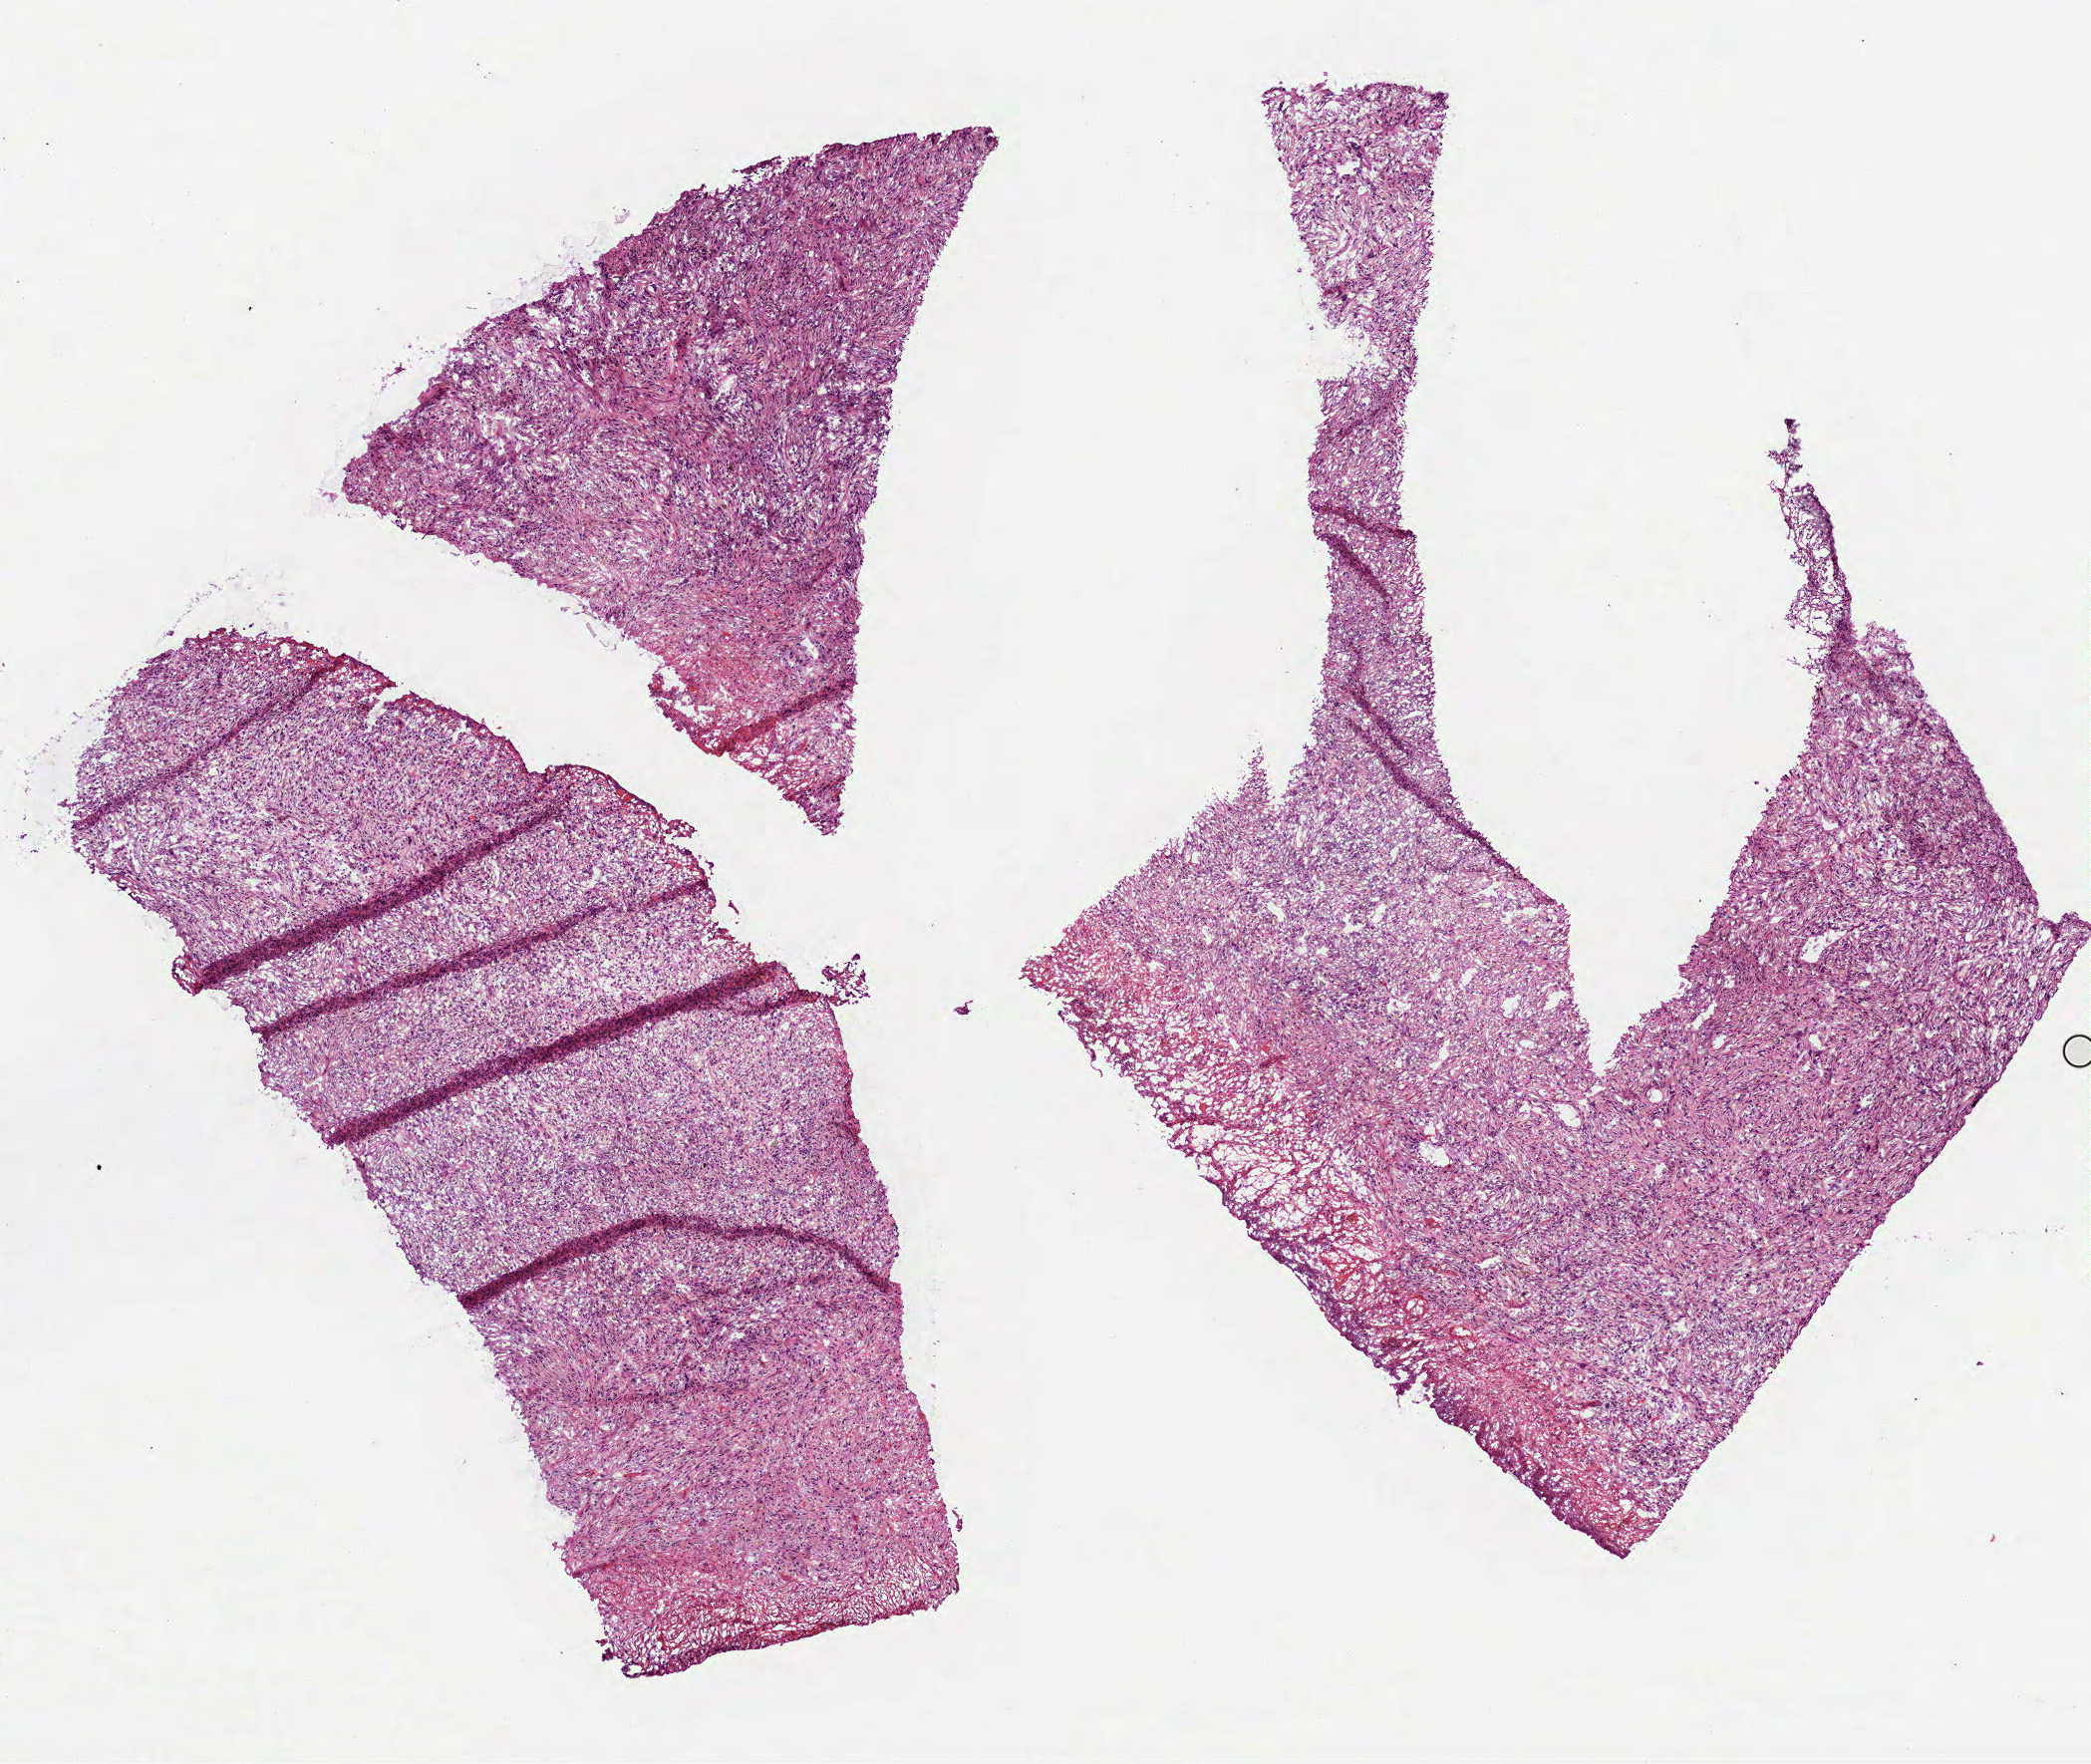
Whole-slide histology image, H&E-stained, shown as a low-resolution overview of the whole scanned area (about 8.5 x 7.1 mm), frozen section, sample: primary tumour, head and neck. Male patient; age at initial diagnosis 79 years. Histologic grade: G3 (poorly differentiated). Pathologist review of this section (percent, as recorded): tumour cells 94%, tumour nuclei 85%, normal cells 0%, stromal cells 5%, necrosis 1%. Inflammatory infiltration, as recorded: lymphocyte infiltration 3%.
* laterality: right
* diagnosis: Squamous cell carcinoma, NOS (tongue, NOS)